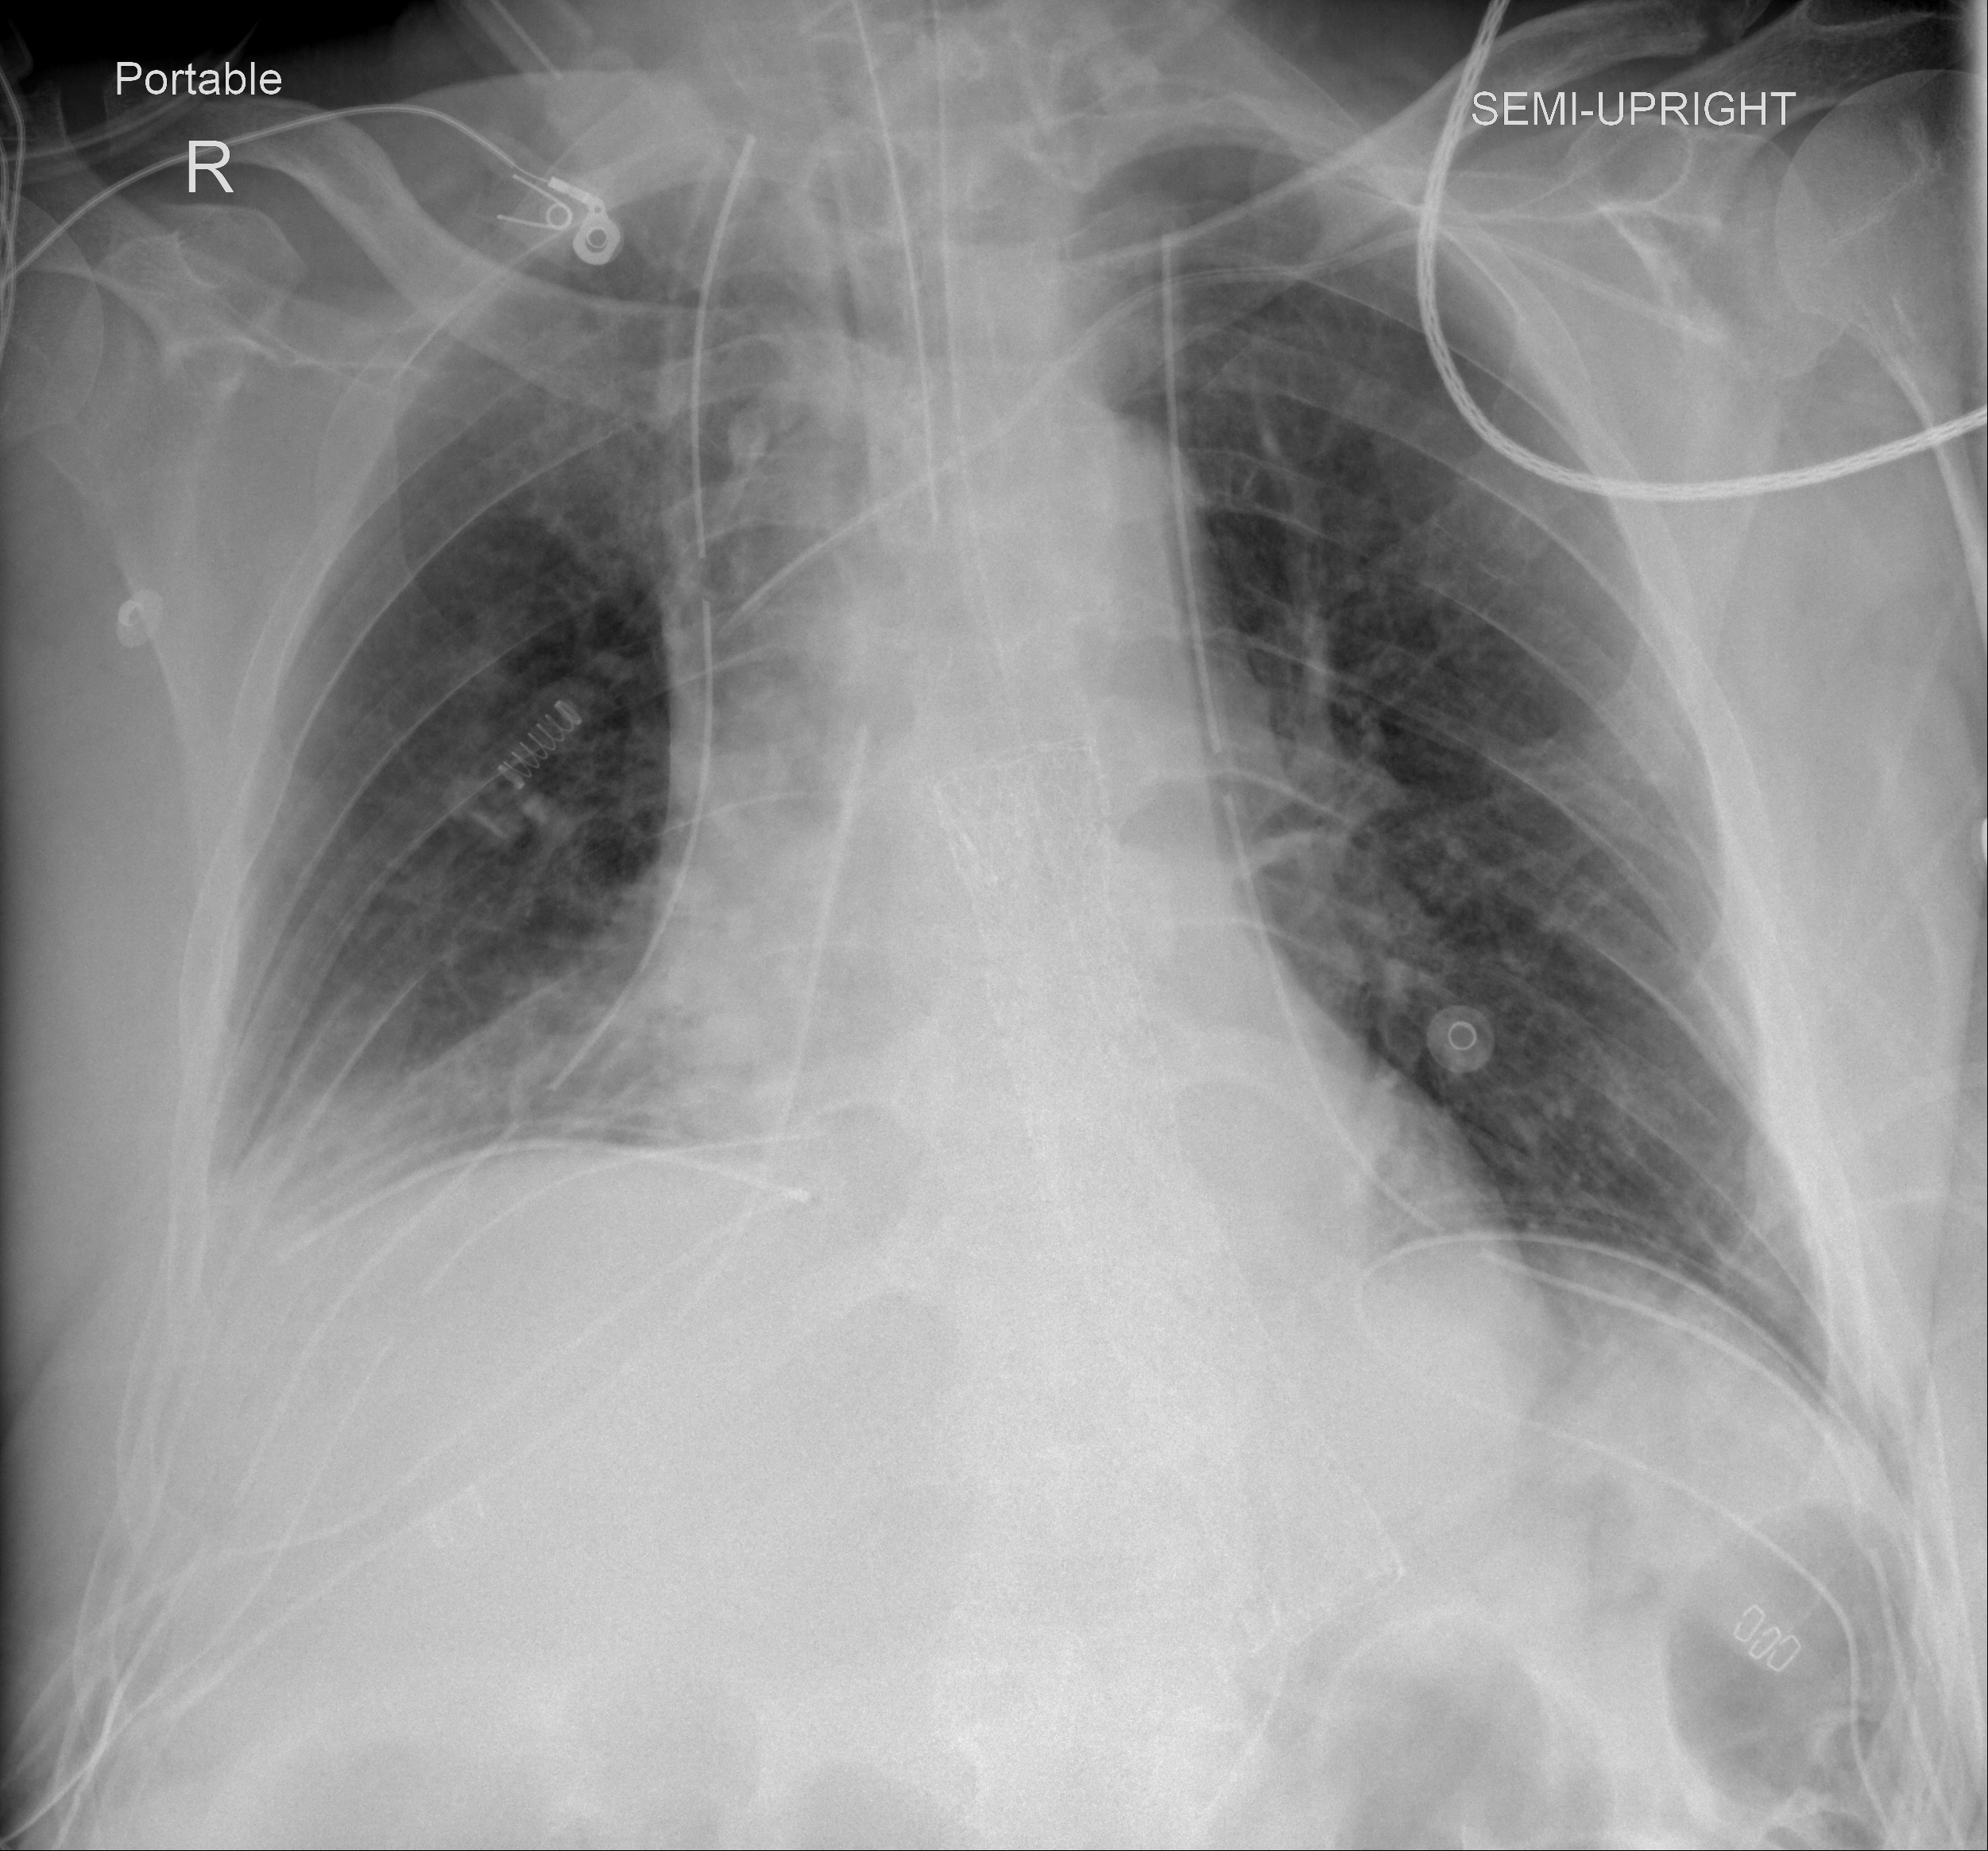
Portable chest radiograph, AP projection. Male patient, age 64 years; imaged 1 day after the COVID-19 diagnosis.
Key findings recorded by the radiologist: Streaky consolidation still present in the lung bases without improvement. There may be some residual pleural fluid mainly on the right side without worsening.